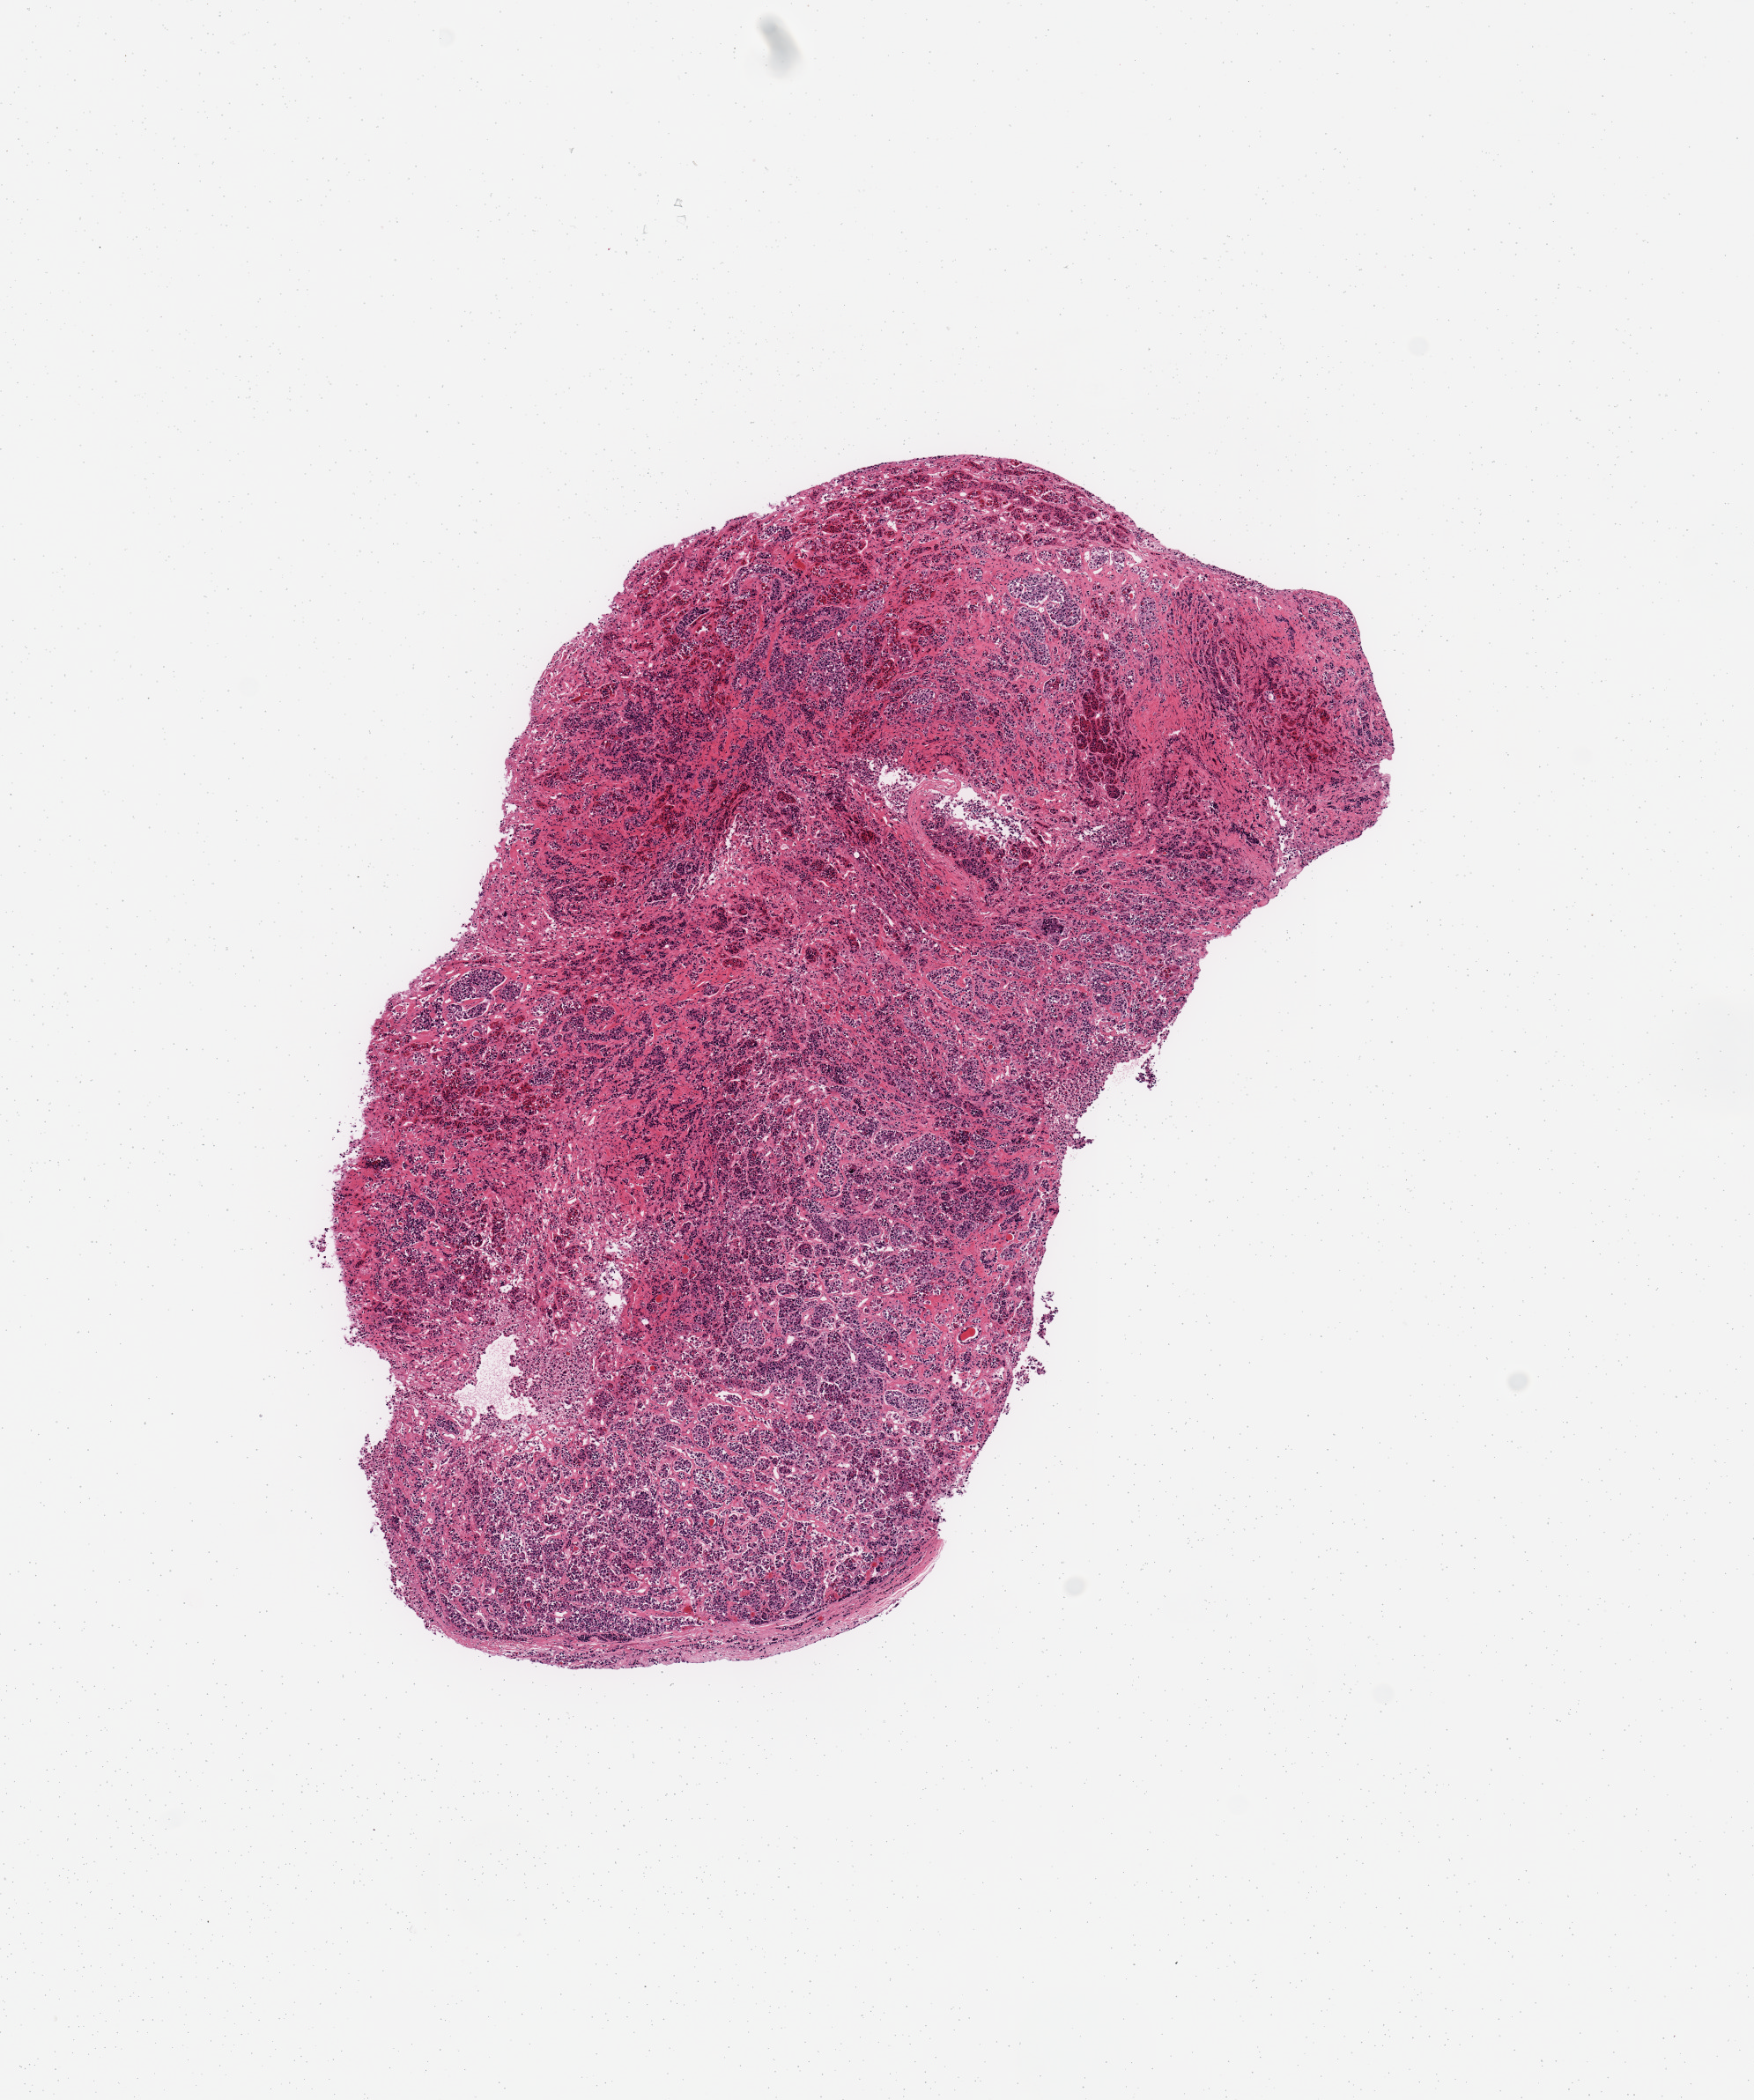
Whole-slide image, H&E stain, whole scanned area (about 7.9 x 9.4 mm, from a 20x scan) shown as a low-resolution overview; PAXgene-fixed paraffin-embedded (PFPE) section; sampled site (target tissue): pituitary; donor tissue sample.
Review note (as recorded): 1 piece; all anterior lobe.